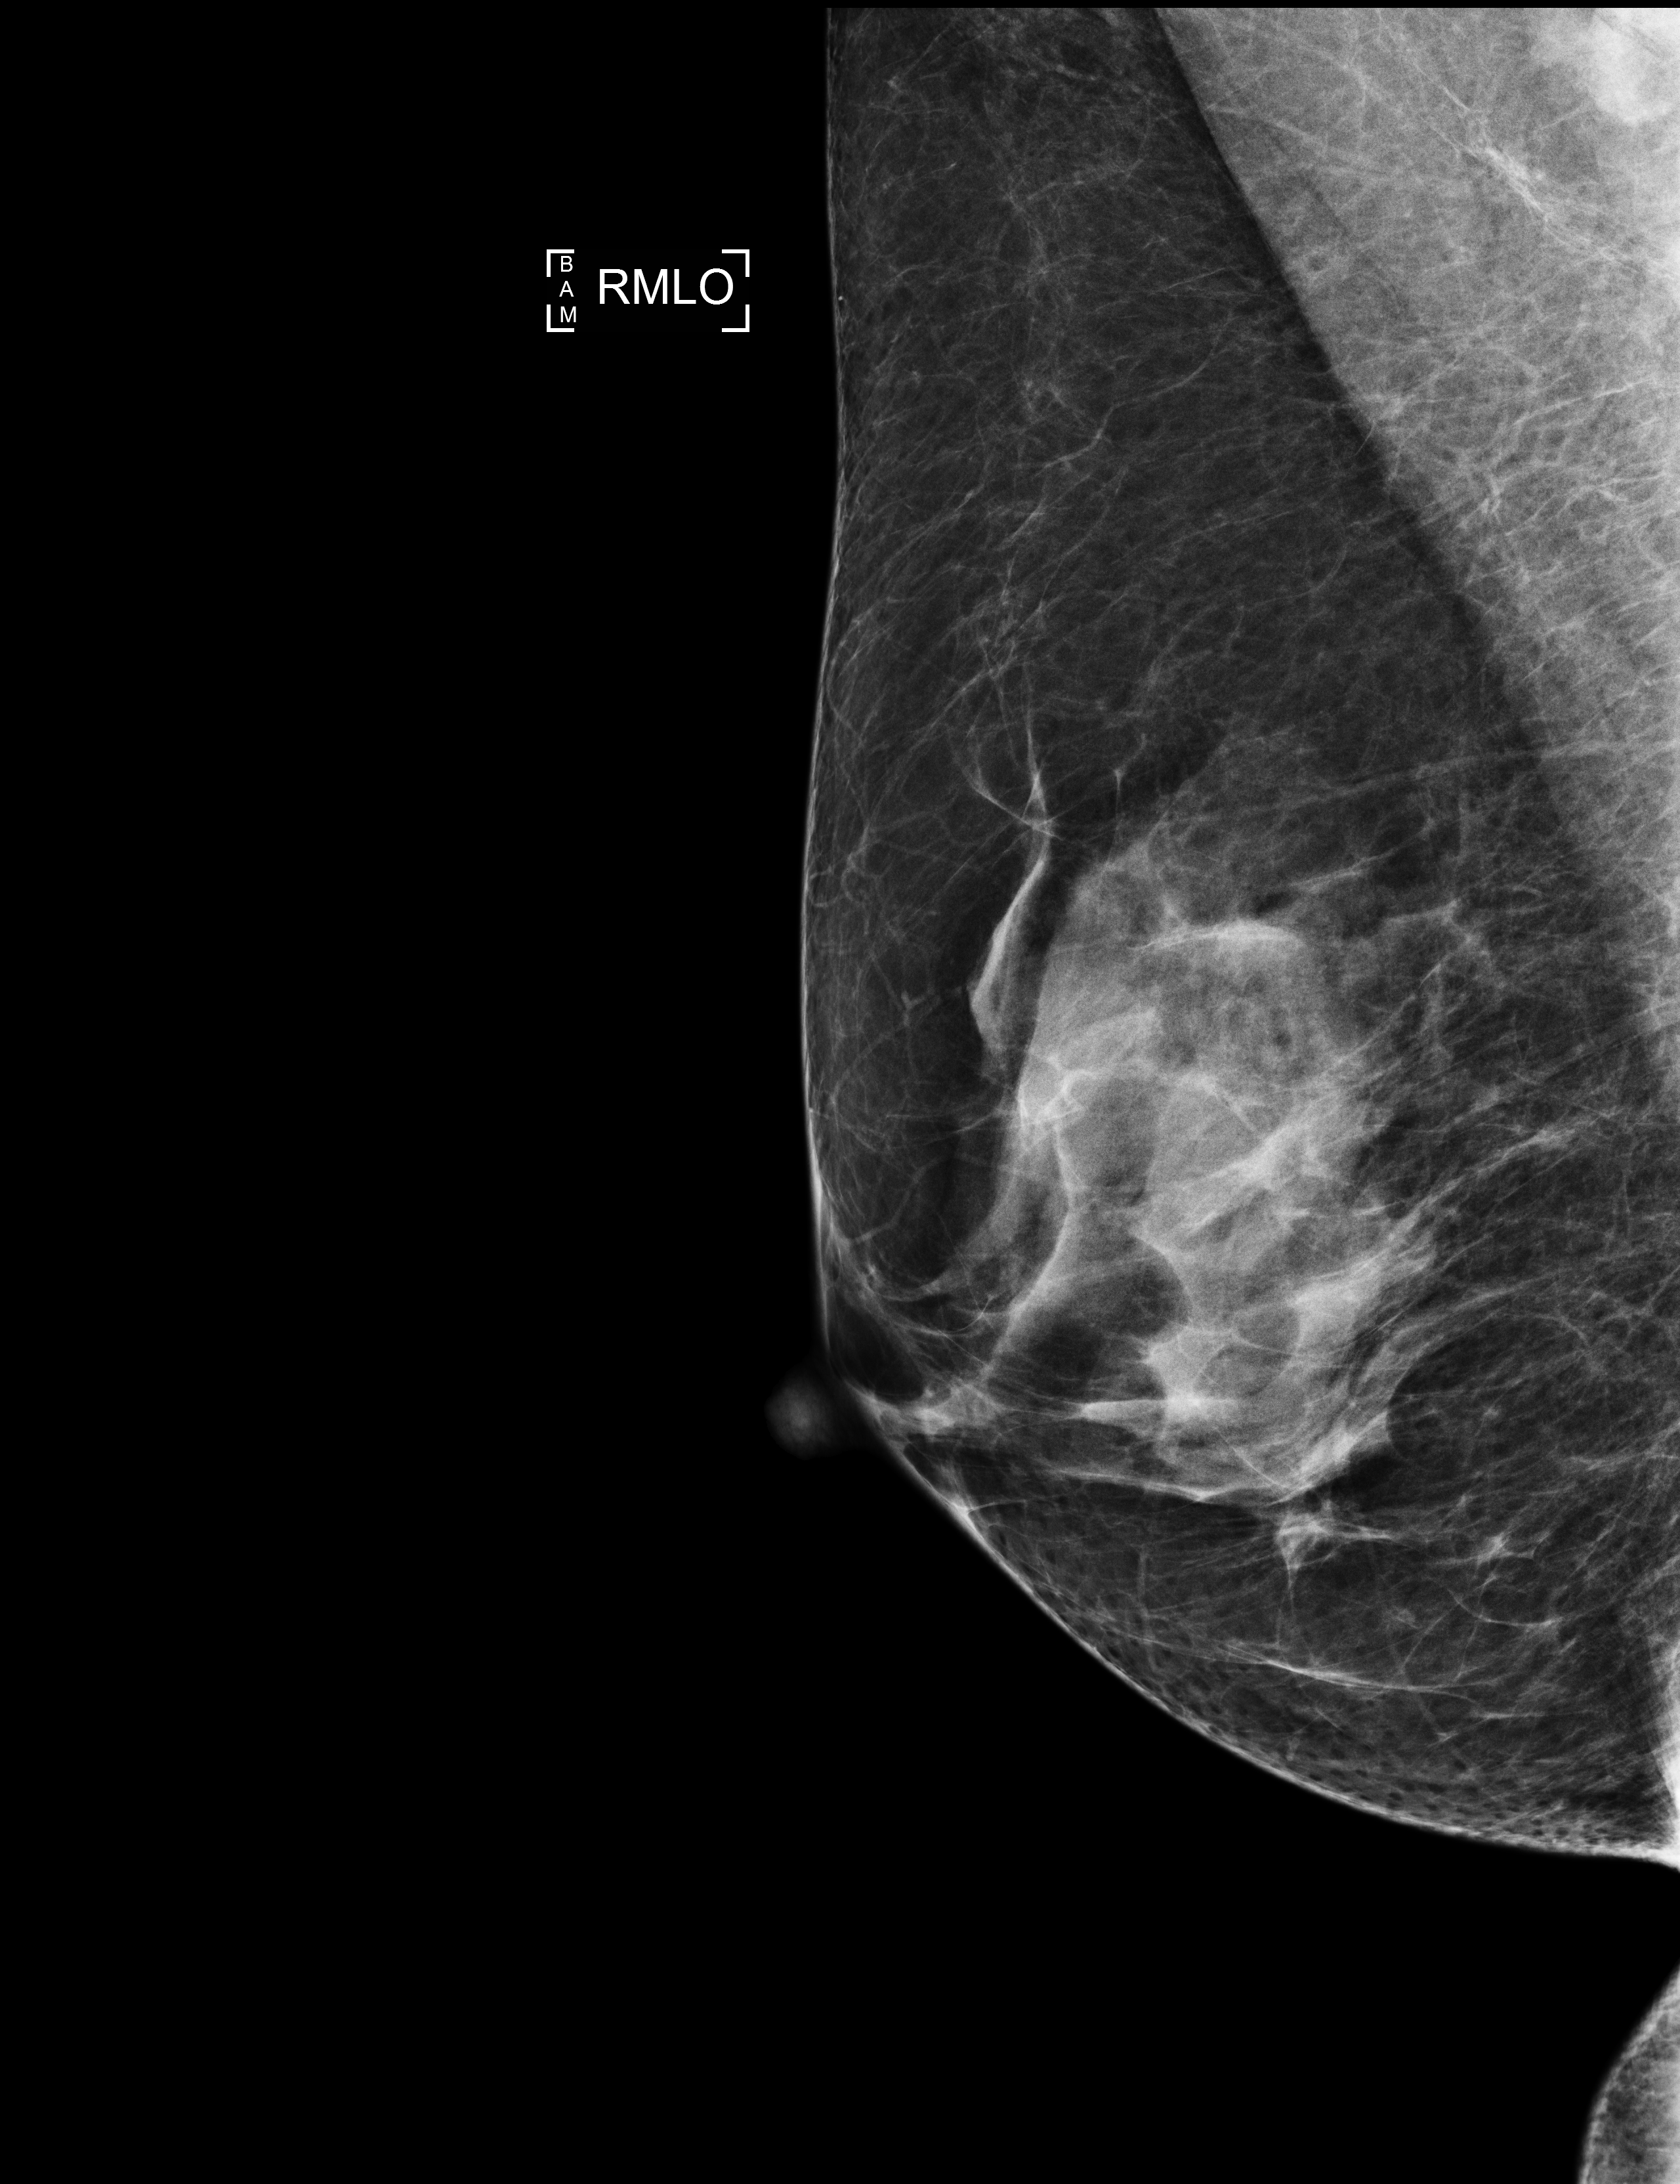
Full-field digital mammogram (FFDM), right breast, MLO view, screening examination, compressed breast thickness 60 mm, system: Selenia Dimensions. Patient: female, 59 years.
BI-RADS breast density category at the screening exam (both breasts, scale 1–4): 3. Final BI-RADS category for the screening round (tomosynthesis exam, both breasts): category 1. Recall: no recall after this screen.